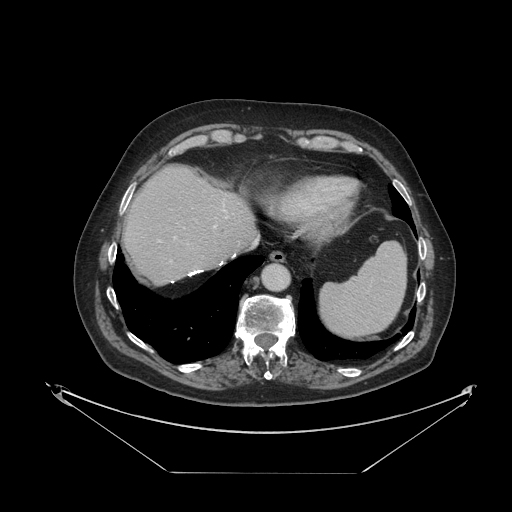
Contrast-enhanced abdominal CT, one axial slice; slice 100 of 121 in the series (ordered by position); reconstruction kernel STANDARD; intravenous contrast given; soft-tissue window (W 400 / L 40 HU); 2.5 mm slice thickness; 512 × 512 image matrix, field of view 500 × 500 mm. Male patient, age 68 years. From the clinical record (not read from this slice): diagnosis: colorectal cancer liver metastases, imaged before liver resection; multiple liver metastases: no; largest metastasis: 4 cm.
Annotated regions visible in this slice (outlined manually by an expert reader):
- hepatic veins: bounding box <175,210,229,238> (left, top, right, bottom; pixels)
- liver: <124,167,255,283>
- planned liver remnant (the part of the liver to remain after resection): <124,166,255,284>
- portal vein (with intrahepatic branches): <158,225,216,263>